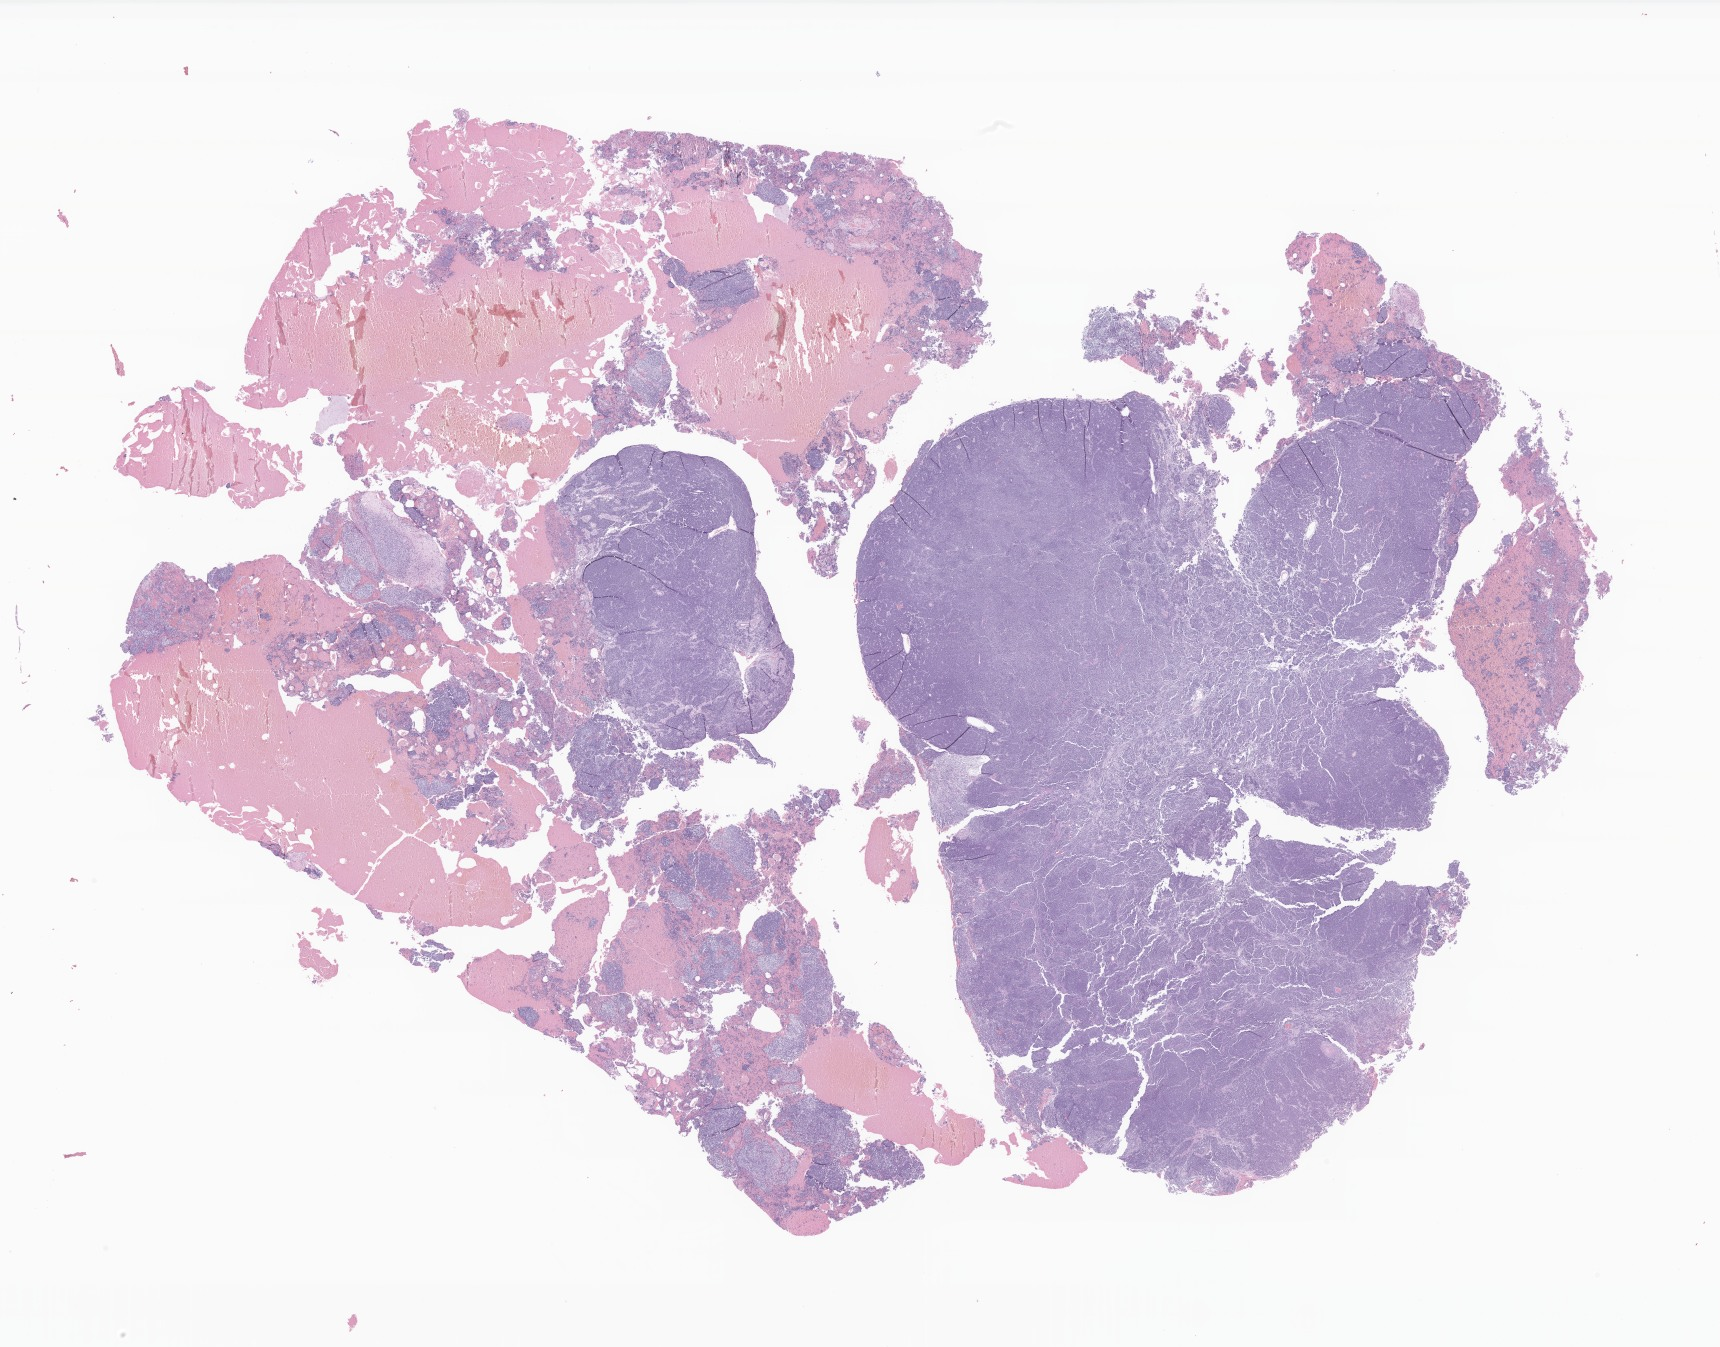
Whole-slide image, hematoxylin and eosin (H&E) stain of tumor tissue from the brain, low-resolution overview of the scanned area, about 29.0 x 22.7 mm. FFPE section. Male patient, age 75 months (6 years 3 months).
- diagnosis: Medulloblastoma, NOS